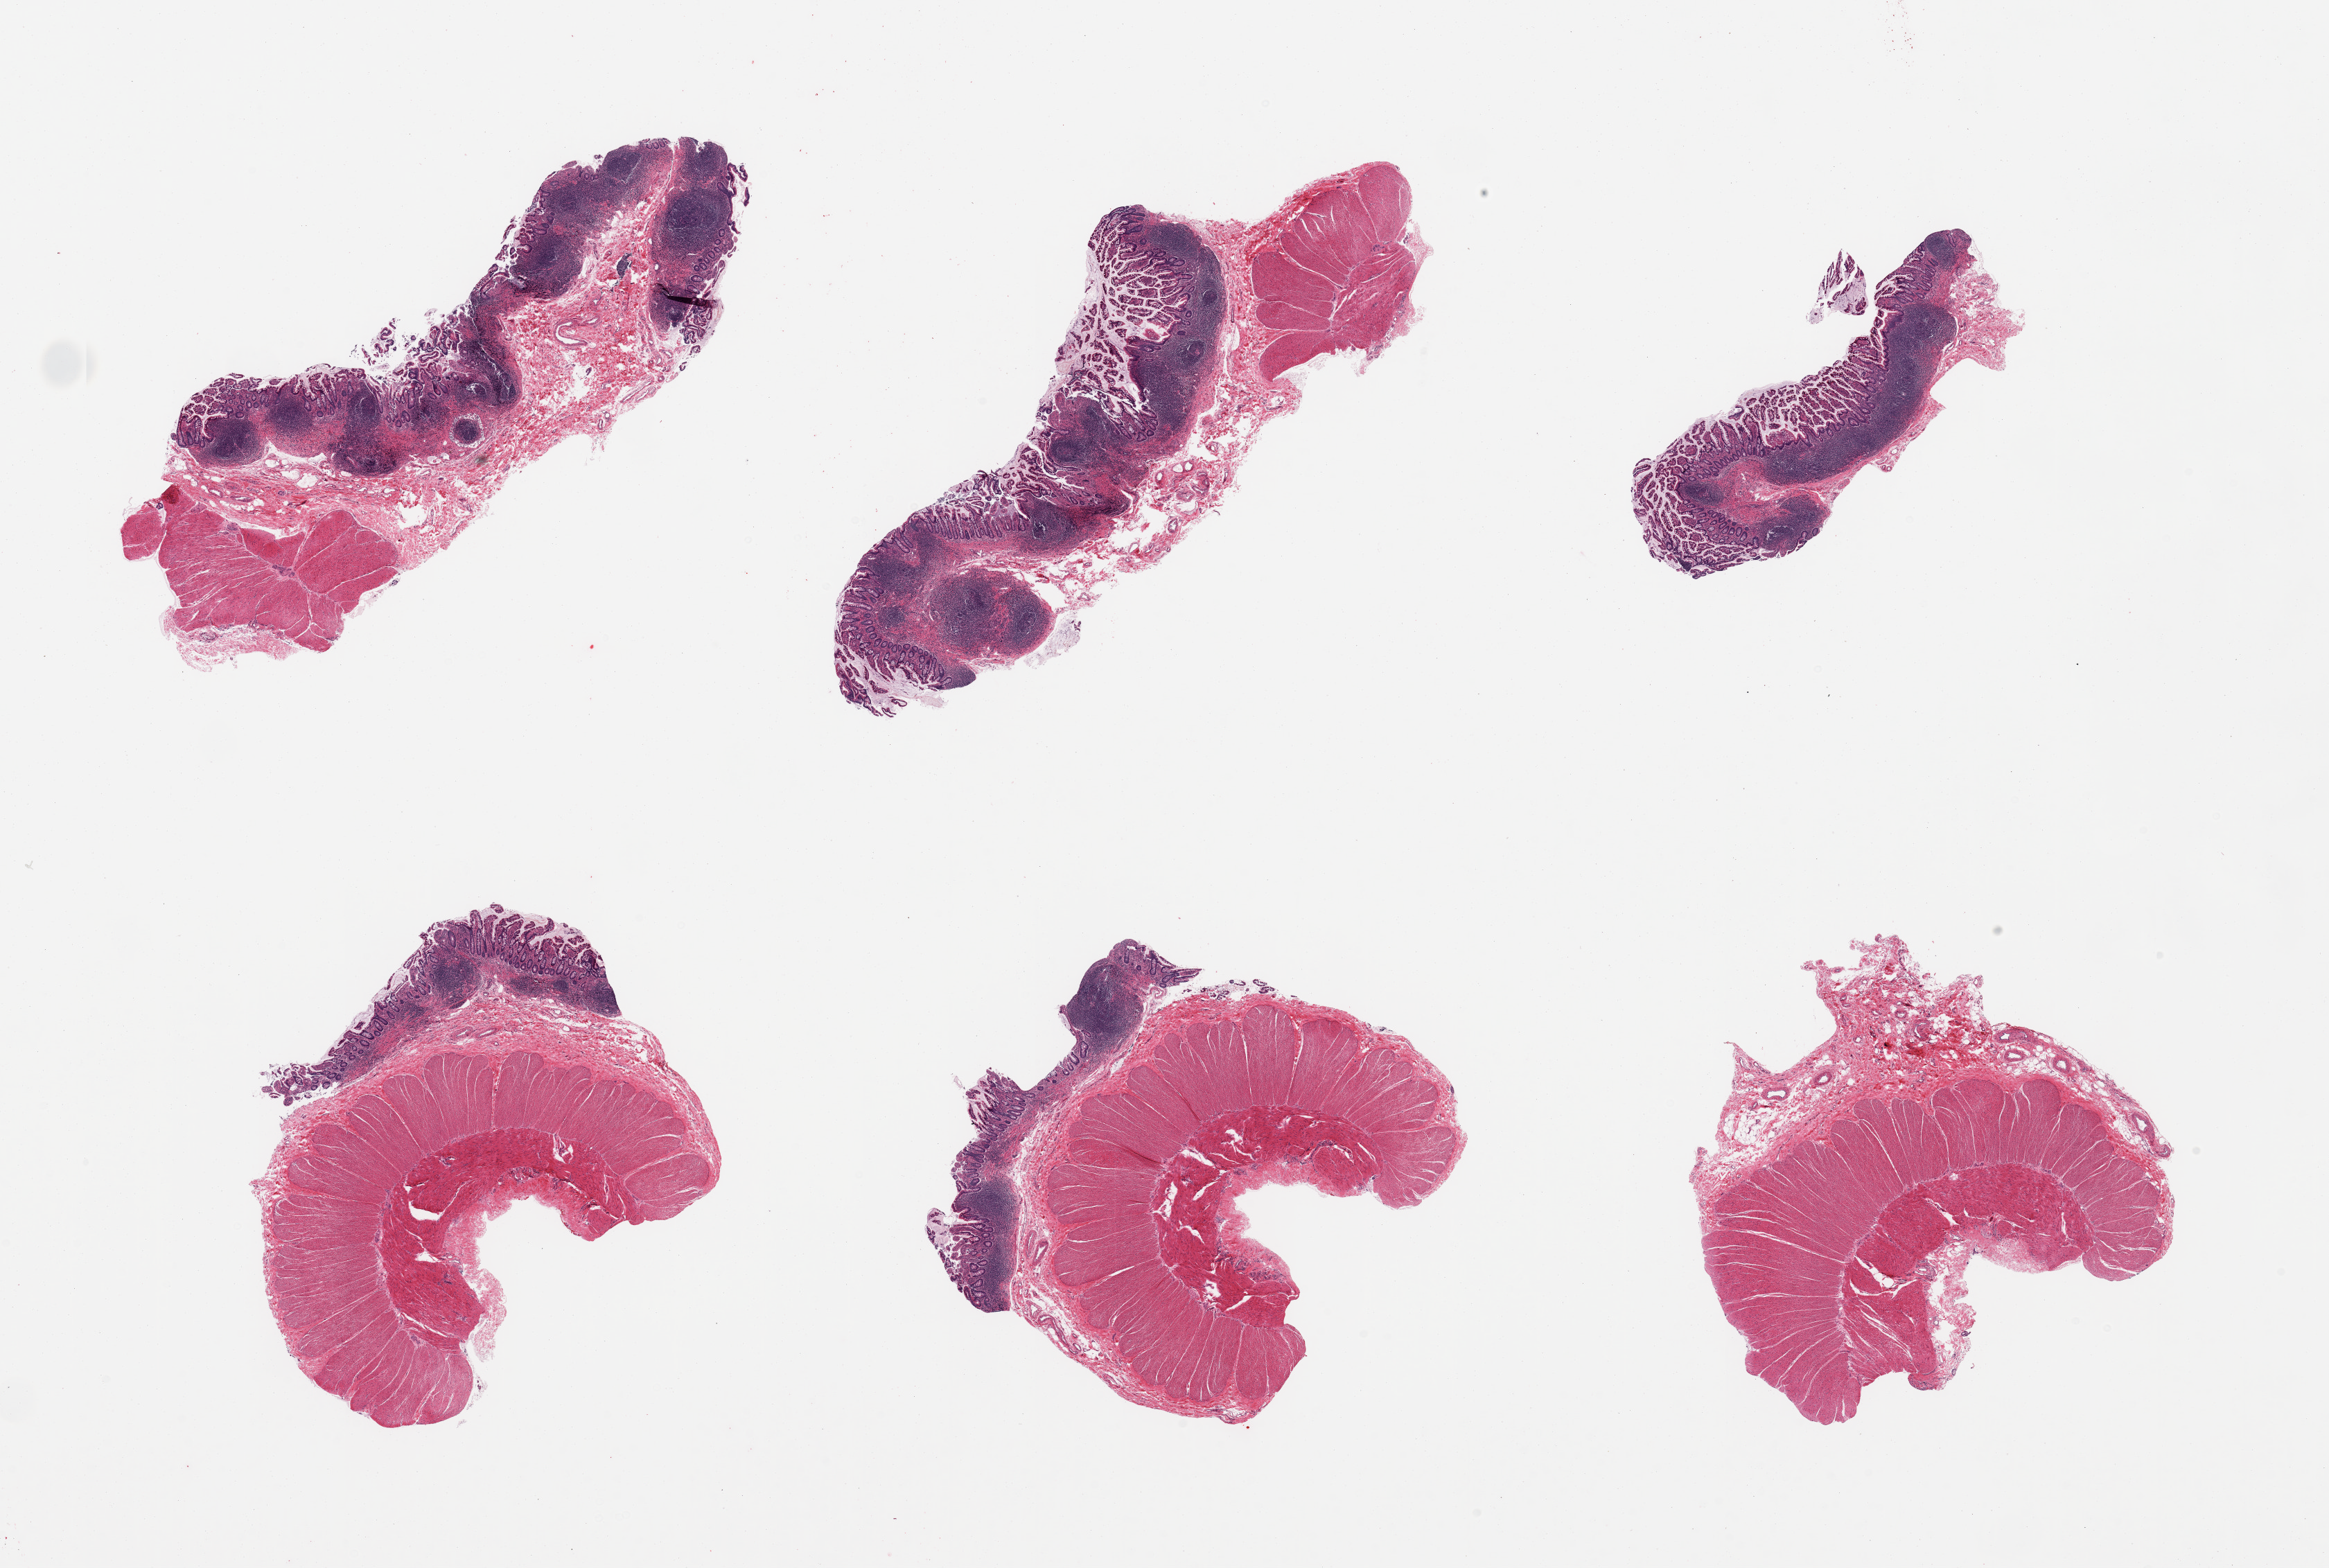
Hematoxylin and eosin (H&E) whole-slide image, low-resolution overview of the scanned area, about 26.6 x 17.9 mm (acquisition: 20x scan). Donor: male.
Specimen: PAXgene-fixed paraffin-embedded (PFPE) section; sampled site (target tissue): ileum; tissue donor sample.